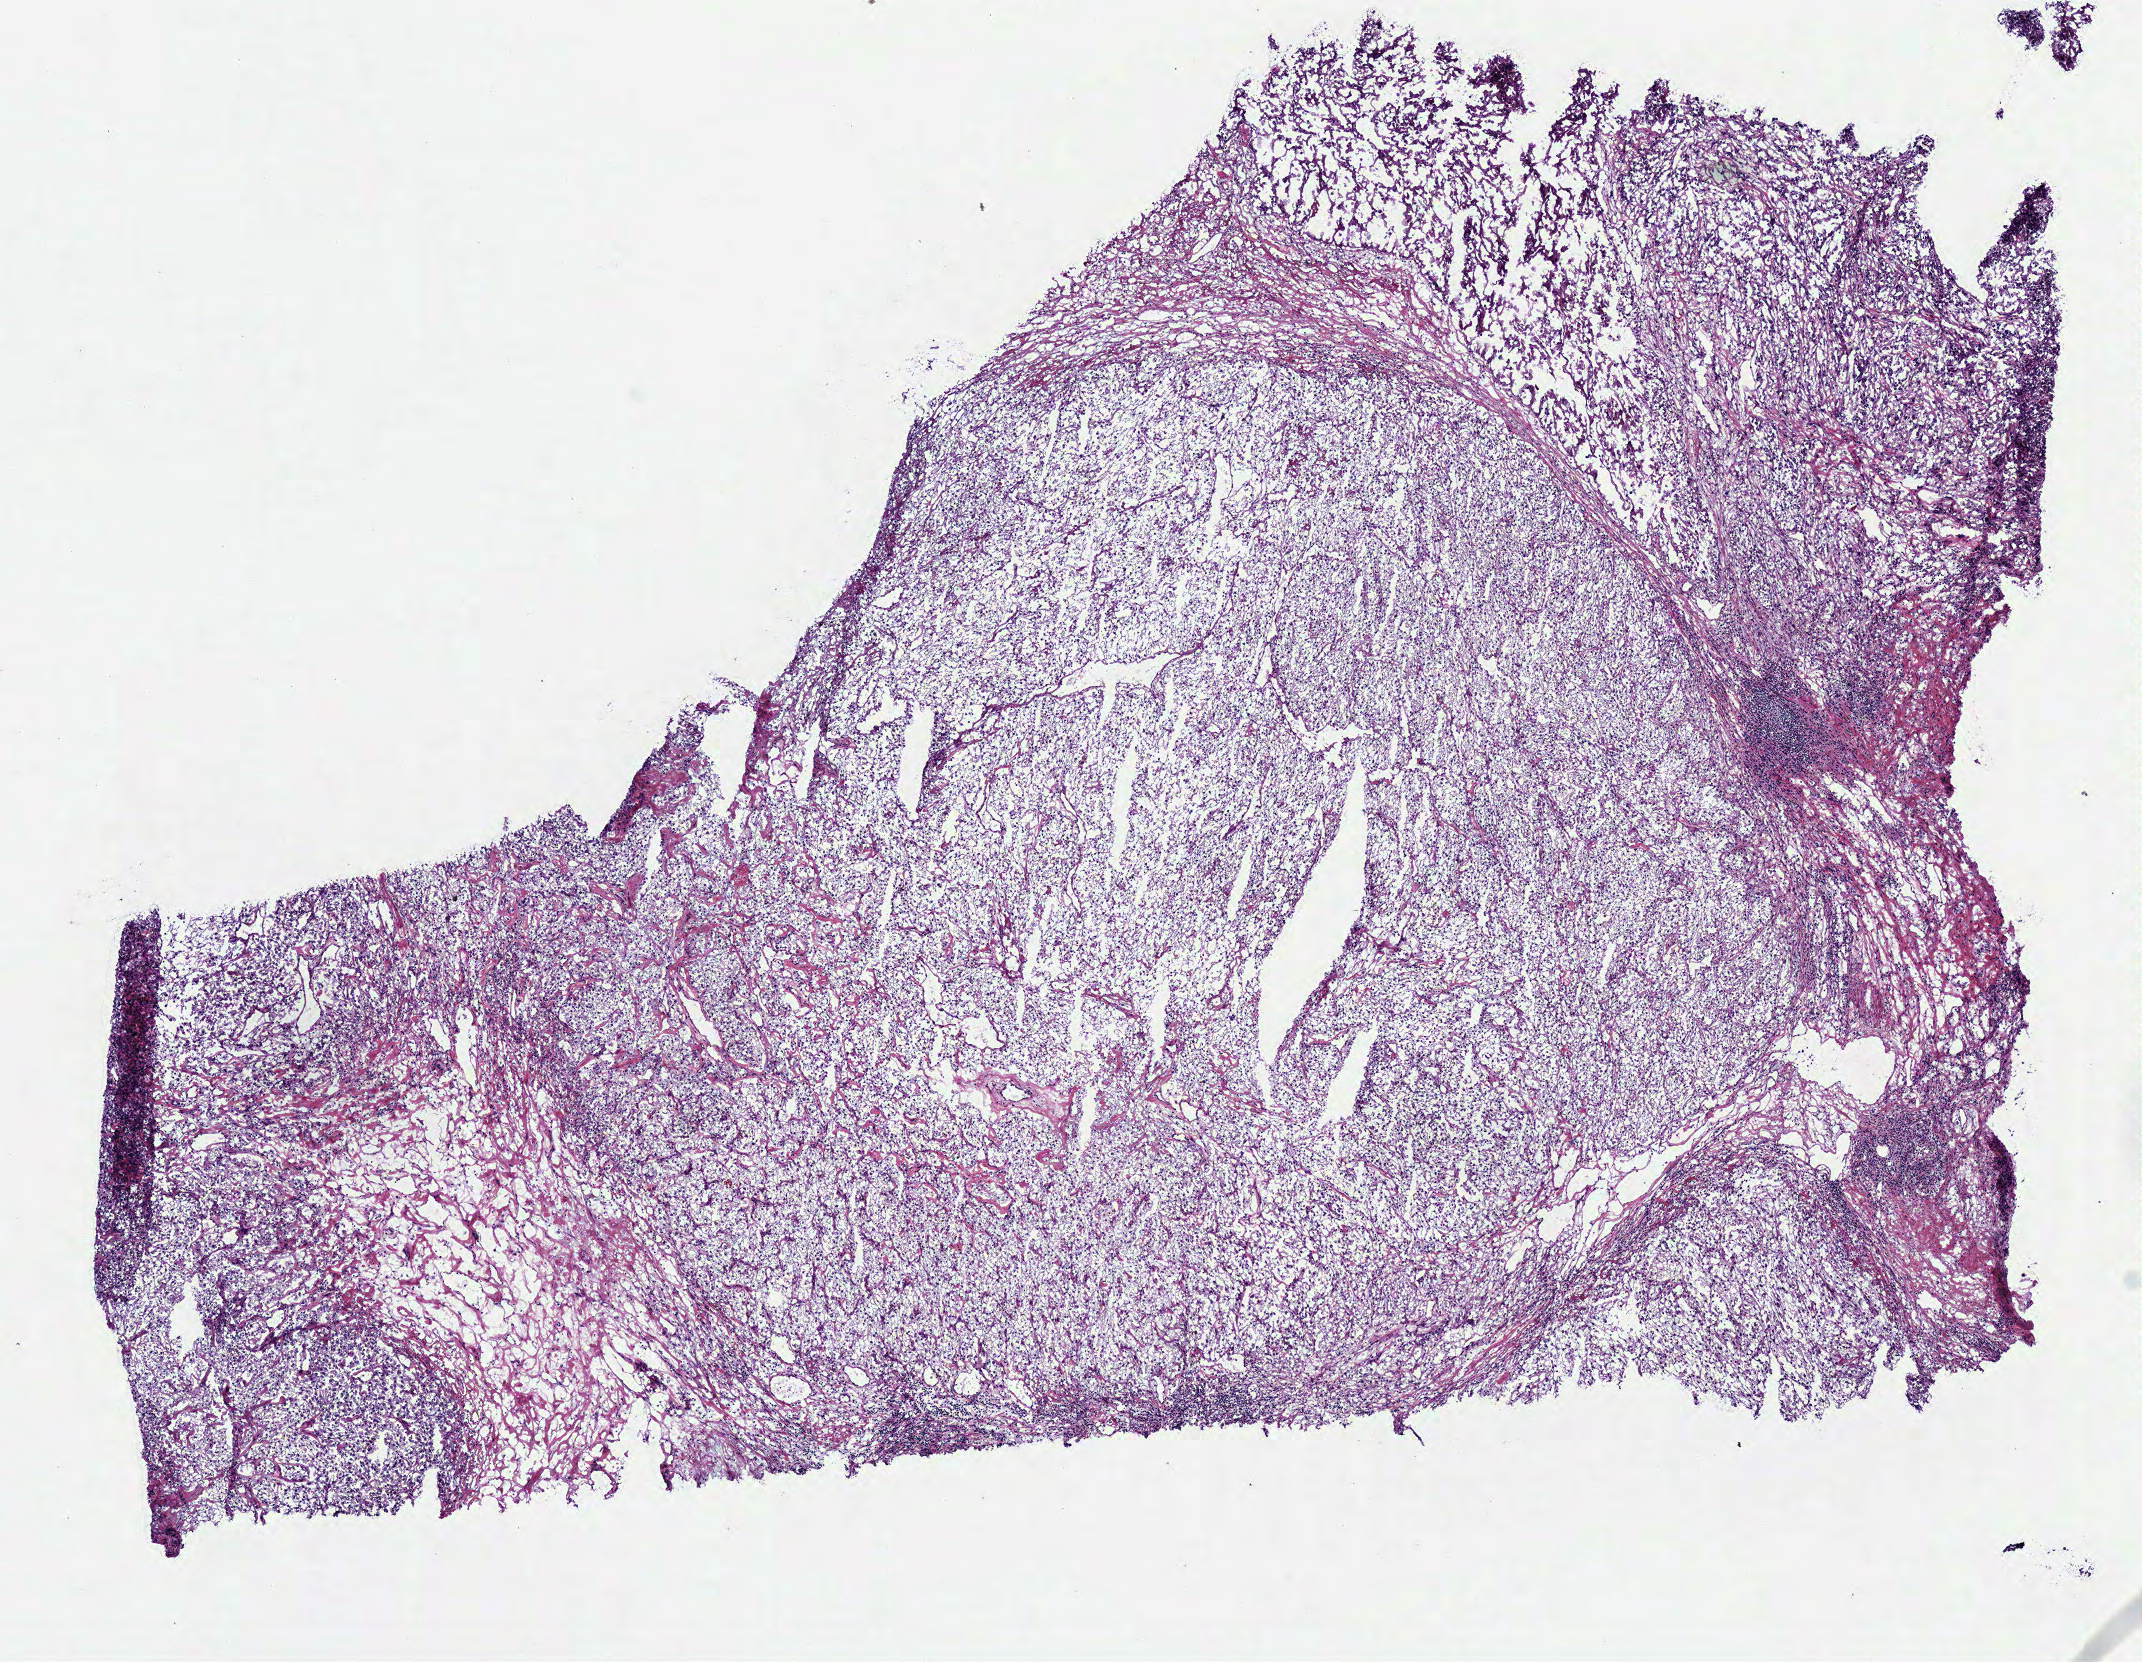
Whole-slide histology image, H&E, shown as a low-resolution overview of the whole scanned area (about 8.4 x 6.5 mm, acquisition: 40x scan), frozen section from the bottom of the tissue portion, sample: primary tumour, kidney. Male, age 32 years at initial diagnosis. Histologic grade: G4 (undifferentiated). Slide review estimates, as recorded: tumour cells 85%, tumour nuclei 80%, normal cells 0%, stromal cells 15%, necrosis 0%.
AJCC pathologic stage: III. Pathologic diagnosis: Clear cell adenocarcinoma, NOS.